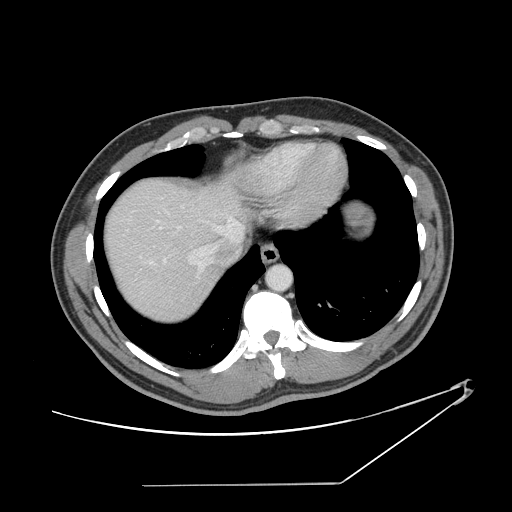
Contrast-enhanced abdominal CT, one axial slice. Position 128 of 152 along the scan axis. 120 kVp. Intravenous contrast given. Soft-tissue window (W 400 / L 40 HU). 2.5 mm slice thickness. 512 × 512 image matrix, field of view 432 × 432 mm. Male patient, age 45 years. Case-level facts recorded for this patient, not image findings: diagnosis: colorectal cancer liver metastases, imaged before liver resection; multiple liver metastases: no; largest metastasis: 1 cm; chemotherapy before resection: yes.
Structures marked on this image (expert manual segmentation):
- hepatic veins: box from (x=127, y=198) to (x=242, y=272) px
- liver: (x=107, y=180)–(x=242, y=319)
- planned liver remnant (the part of the liver to remain after resection): (x=107, y=181)–(x=230, y=320)